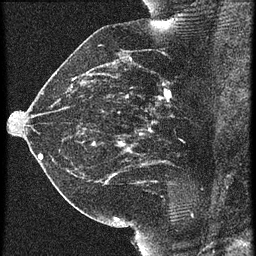
Breast MRI (dynamic contrast-enhanced), one sagittal slice; 3 images stored at this slice position (order not interpretable as contrast timing); 1.5 T; TE 4.2 ms, TR 21.3 ms; 256 × 256 image matrix, field of view 180 × 180 mm. Female patient, age 42 years. Case-level facts recorded for this patient, not image findings: setting: breast cancer imaged before/during neoadjuvant chemotherapy; receptor status: HER2-positive.
Annotated regions visible in this slice (semi-automatic segmentation, software-assisted and operator-edited):
- analysis volume of interest (the breast-tissue region the enhancement analysis was run in; not a lesion): bounding box [x1, y1, x2, y2] px = [122, 82, 195, 147]
- tumour enhancement mask (voxels above the 90 % enhancement threshold inside the analysis volume of interest): [122, 90, 171, 145]